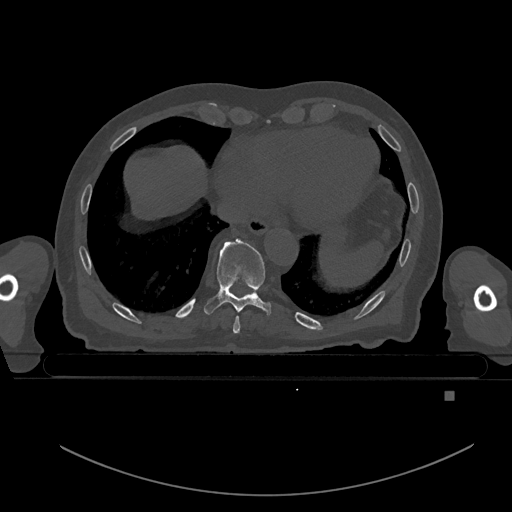
CT including the spine, one axial slice. Slice 148 of 969 in the series (ordered by position). Bone window (W 1800 / L 400 HU). 512 × 512 image matrix, field of view 456 × 456 mm. Male patient, age 82 years. Case-level facts recorded for this patient, not image findings: primary cancer: prostate; vertebrae with lytic lesions (as recorded): T11, T9, T8, T2.
Outlined on this slice (semi-automatically segmented with operator editing):
- T8 vertebra: box from (x=233, y=316) to (x=240, y=333) px
- T9 vertebra: (x=204, y=239)–(x=272, y=317)